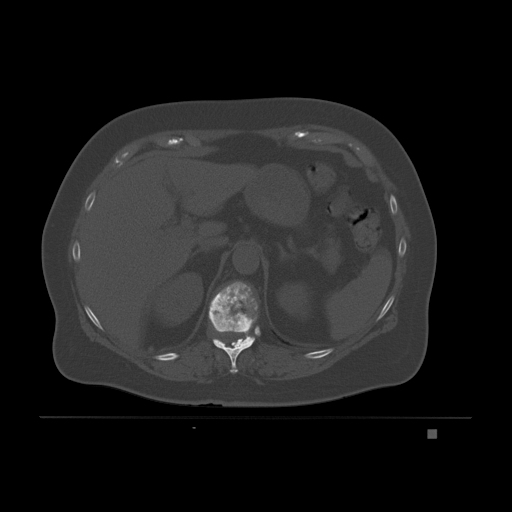
CT including the spine, one axial slice. Position 95 of 221 along the scan axis. Bone window (W 1800 / L 400 HU). 3 mm slice thickness. 512 × 512 image matrix, field of view 474 × 474 mm. Female patient, age 63 years. From the clinical record (not read from this slice): primary cancer: breast.
Structures marked on this image (semi-automatically segmented with operator editing):
- T10 vertebra: box from (x=213, y=339) to (x=252, y=373) px
- T11 vertebra: (x=209, y=281)–(x=258, y=346)